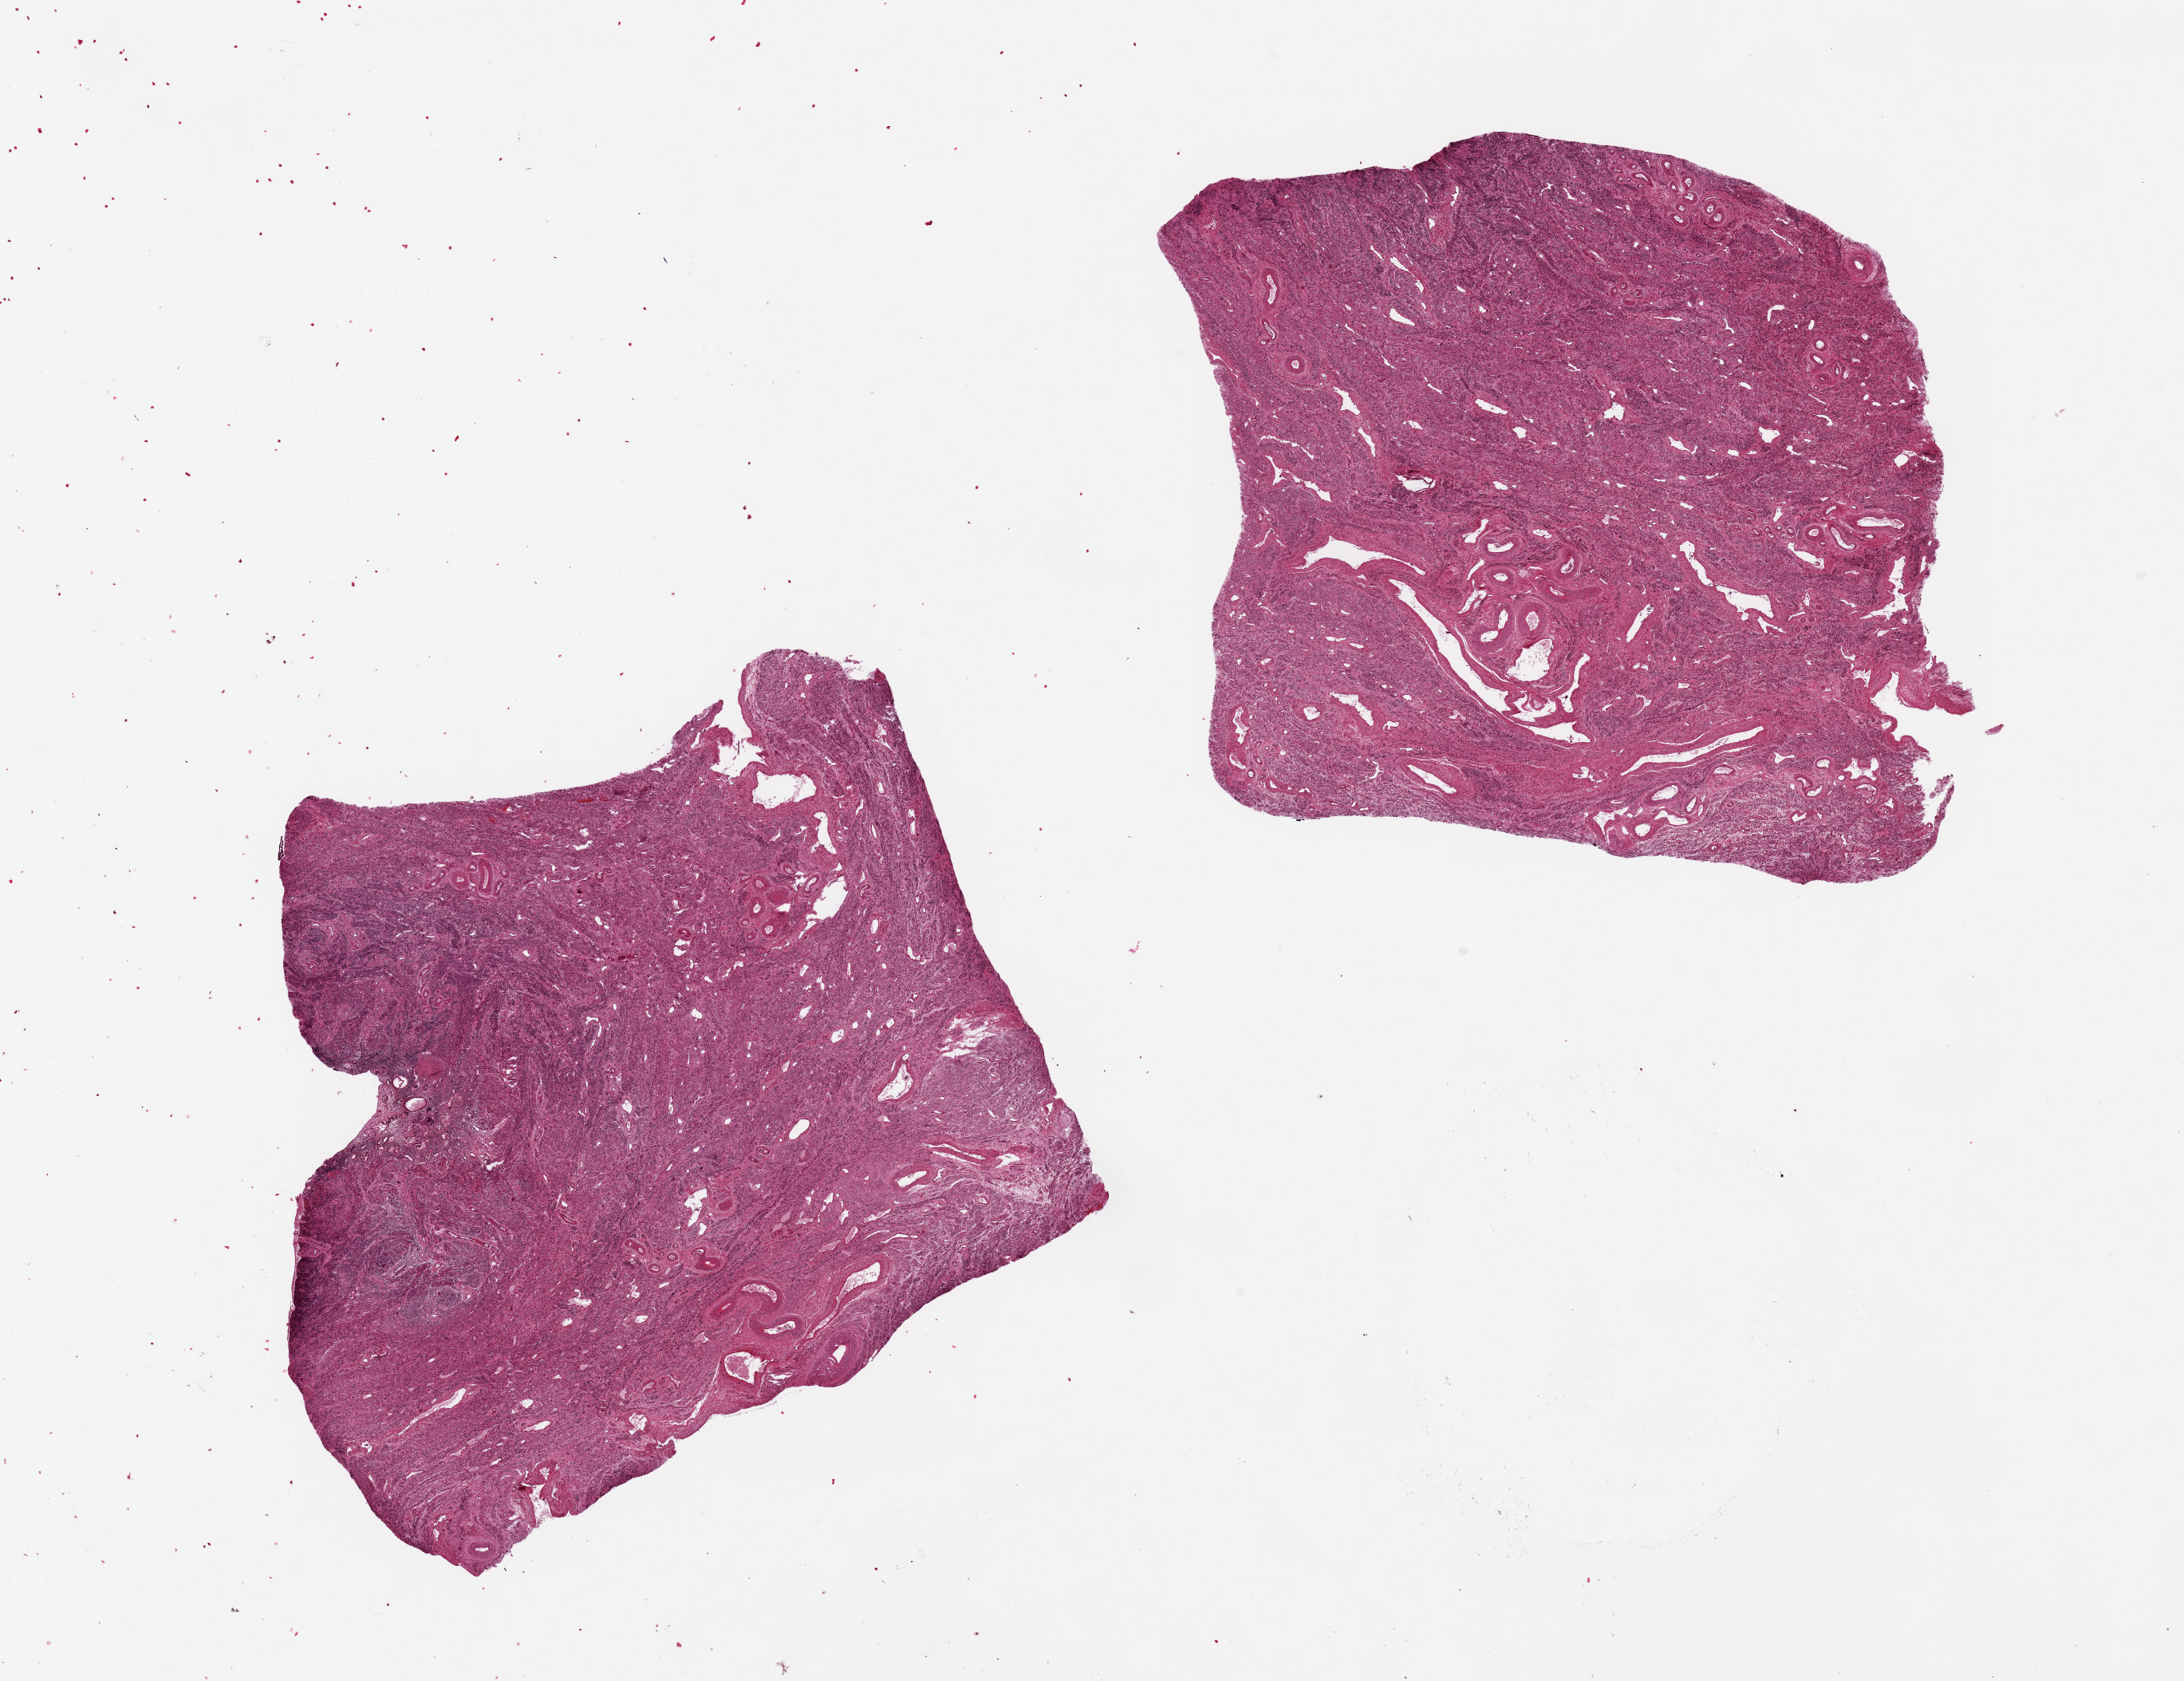
Hematoxylin and eosin (H&E) whole-slide image, low-resolution overview of the scanned area, about 21.7 x 16.7 mm (slide scanned at 20x), PAXgene-fixed paraffin-embedded (PFPE) section, target tissue: uterus, tissue donor sample.
* review note (as recorded): 2 pieces 8x6 & 7x6 mm; all myometrium